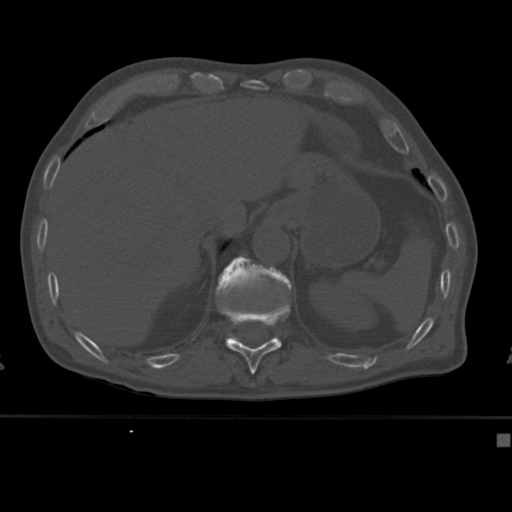
CT including the spine, one axial slice. Position 205 of 430 along the scan axis. 120 kVp. Bone window (W 1800 / L 400 HU). 1.5 mm slice thickness. 512 × 512 image matrix, field of view 337 × 337 mm. Male patient, age 64 years. Case-level facts recorded for this patient, not image findings: primary cancer: uterus; vertebrae with lytic lesions (as recorded): T1, T4, T5, T7, L5.
Annotated regions visible in this slice (semi-automatically segmented with operator editing):
- T11 vertebra: bounding box <218,299,290,374> (left, top, right, bottom; pixels)
- T12 vertebra: <215,256,291,339>